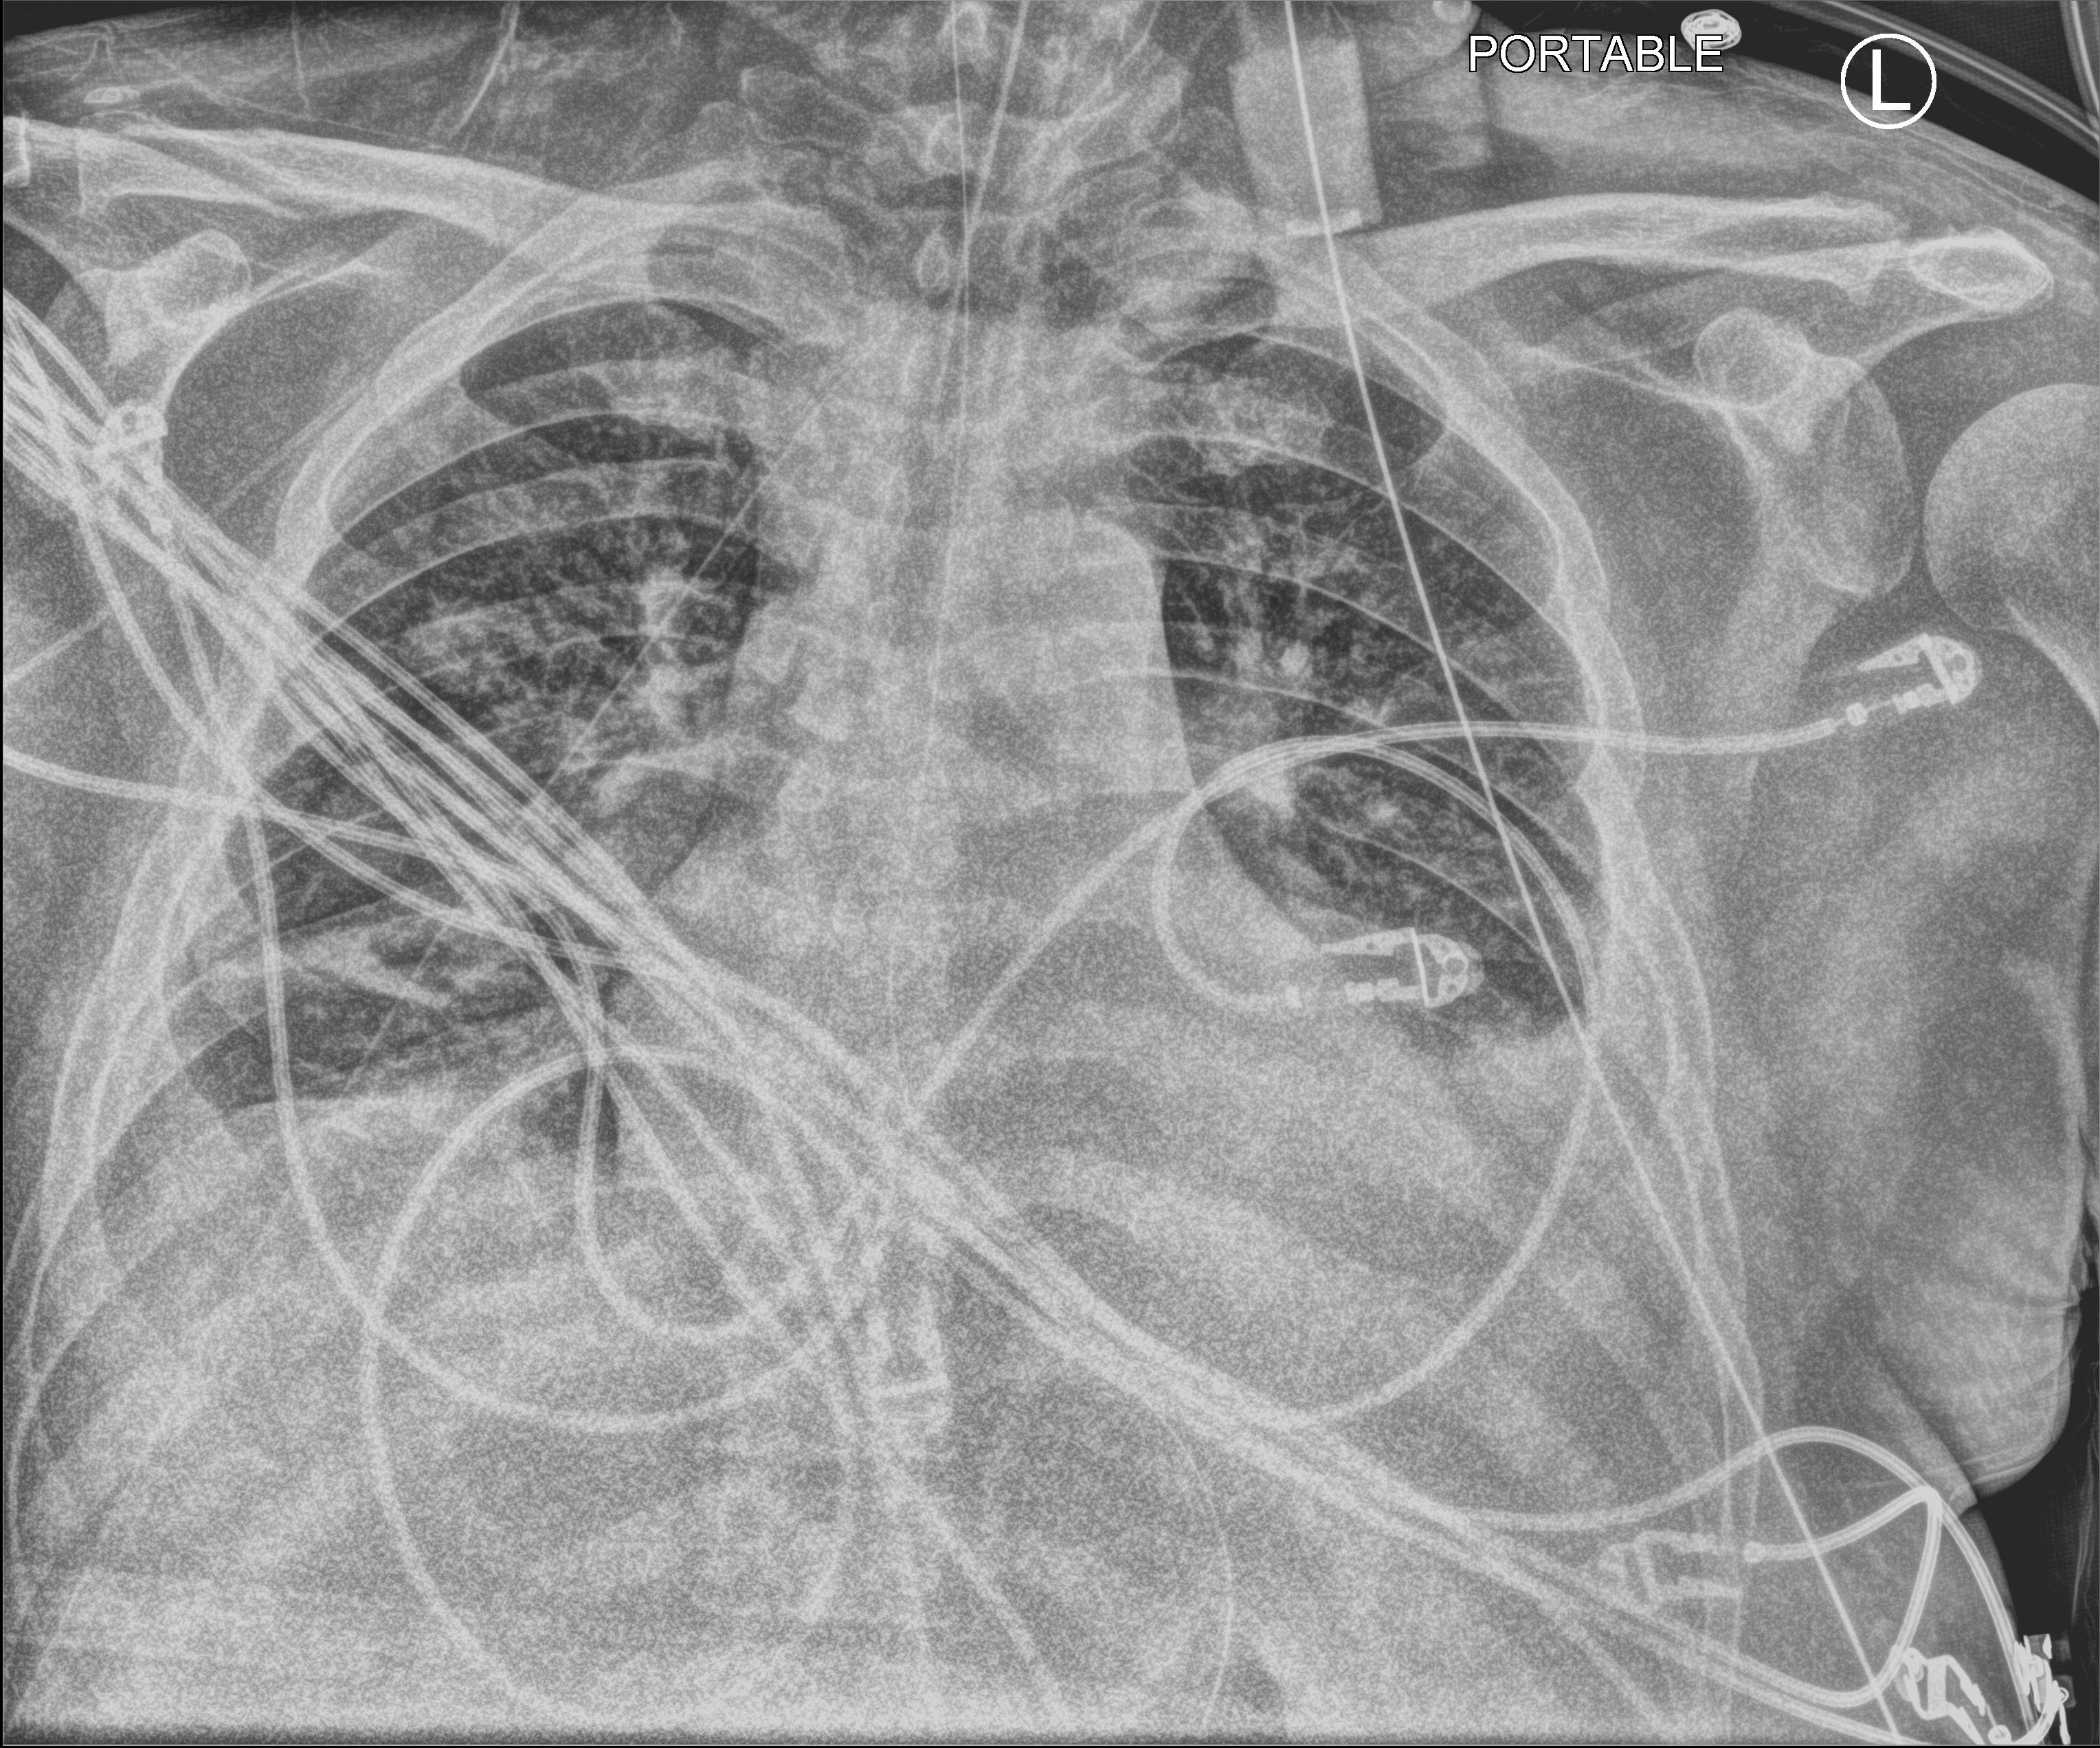
Bedside chest radiograph (computed radiography); anteroposterior (AP) projection. Male patient hospitalised with COVID-19, age 18–59 years.
Admission-level facts for this patient (not findings on this image; timing relative to this image not recorded):
- admitted to intensive care during this hospital stay: yes
- mechanically ventilated during this hospital stay: yes